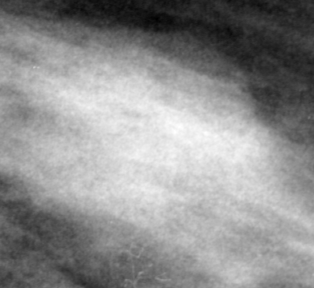
Cropped region of a digitized screen-film mammogram centred on a radiologist-marked abnormality; left breast; CC view.
Marked abnormality: mass, shape lobulated, margins obscured; BI-RADS assessment category 4; subtlety rating 3 on a 1 (subtle) to 5 (obvious) scale; pathology result (as recorded, not read from the image): malignant.